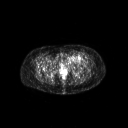
FDG PET of an extremity soft-tissue mass (from a PET/CT study), one axial slice; position 46 of 267 along the scan axis; 3.27 mm slice thickness; 128 × 128 image matrix, field of view 700 × 700 mm. Patient: female, 47 years. Case-level facts recorded for this patient, not image findings: histological type: myxofibrosarcoma; grade: intermediate; site of the primary tumour: left thigh.
Annotated regions visible in this slice (expert contour drawn on MRI and transferred to this co-registered scan by the dataset authors):
- gross tumour volume including surrounding oedema: bounding box [x1, y1, x2, y2] px = [65, 54, 84, 63]
- gross tumour volume (mass): [72, 55, 76, 59]